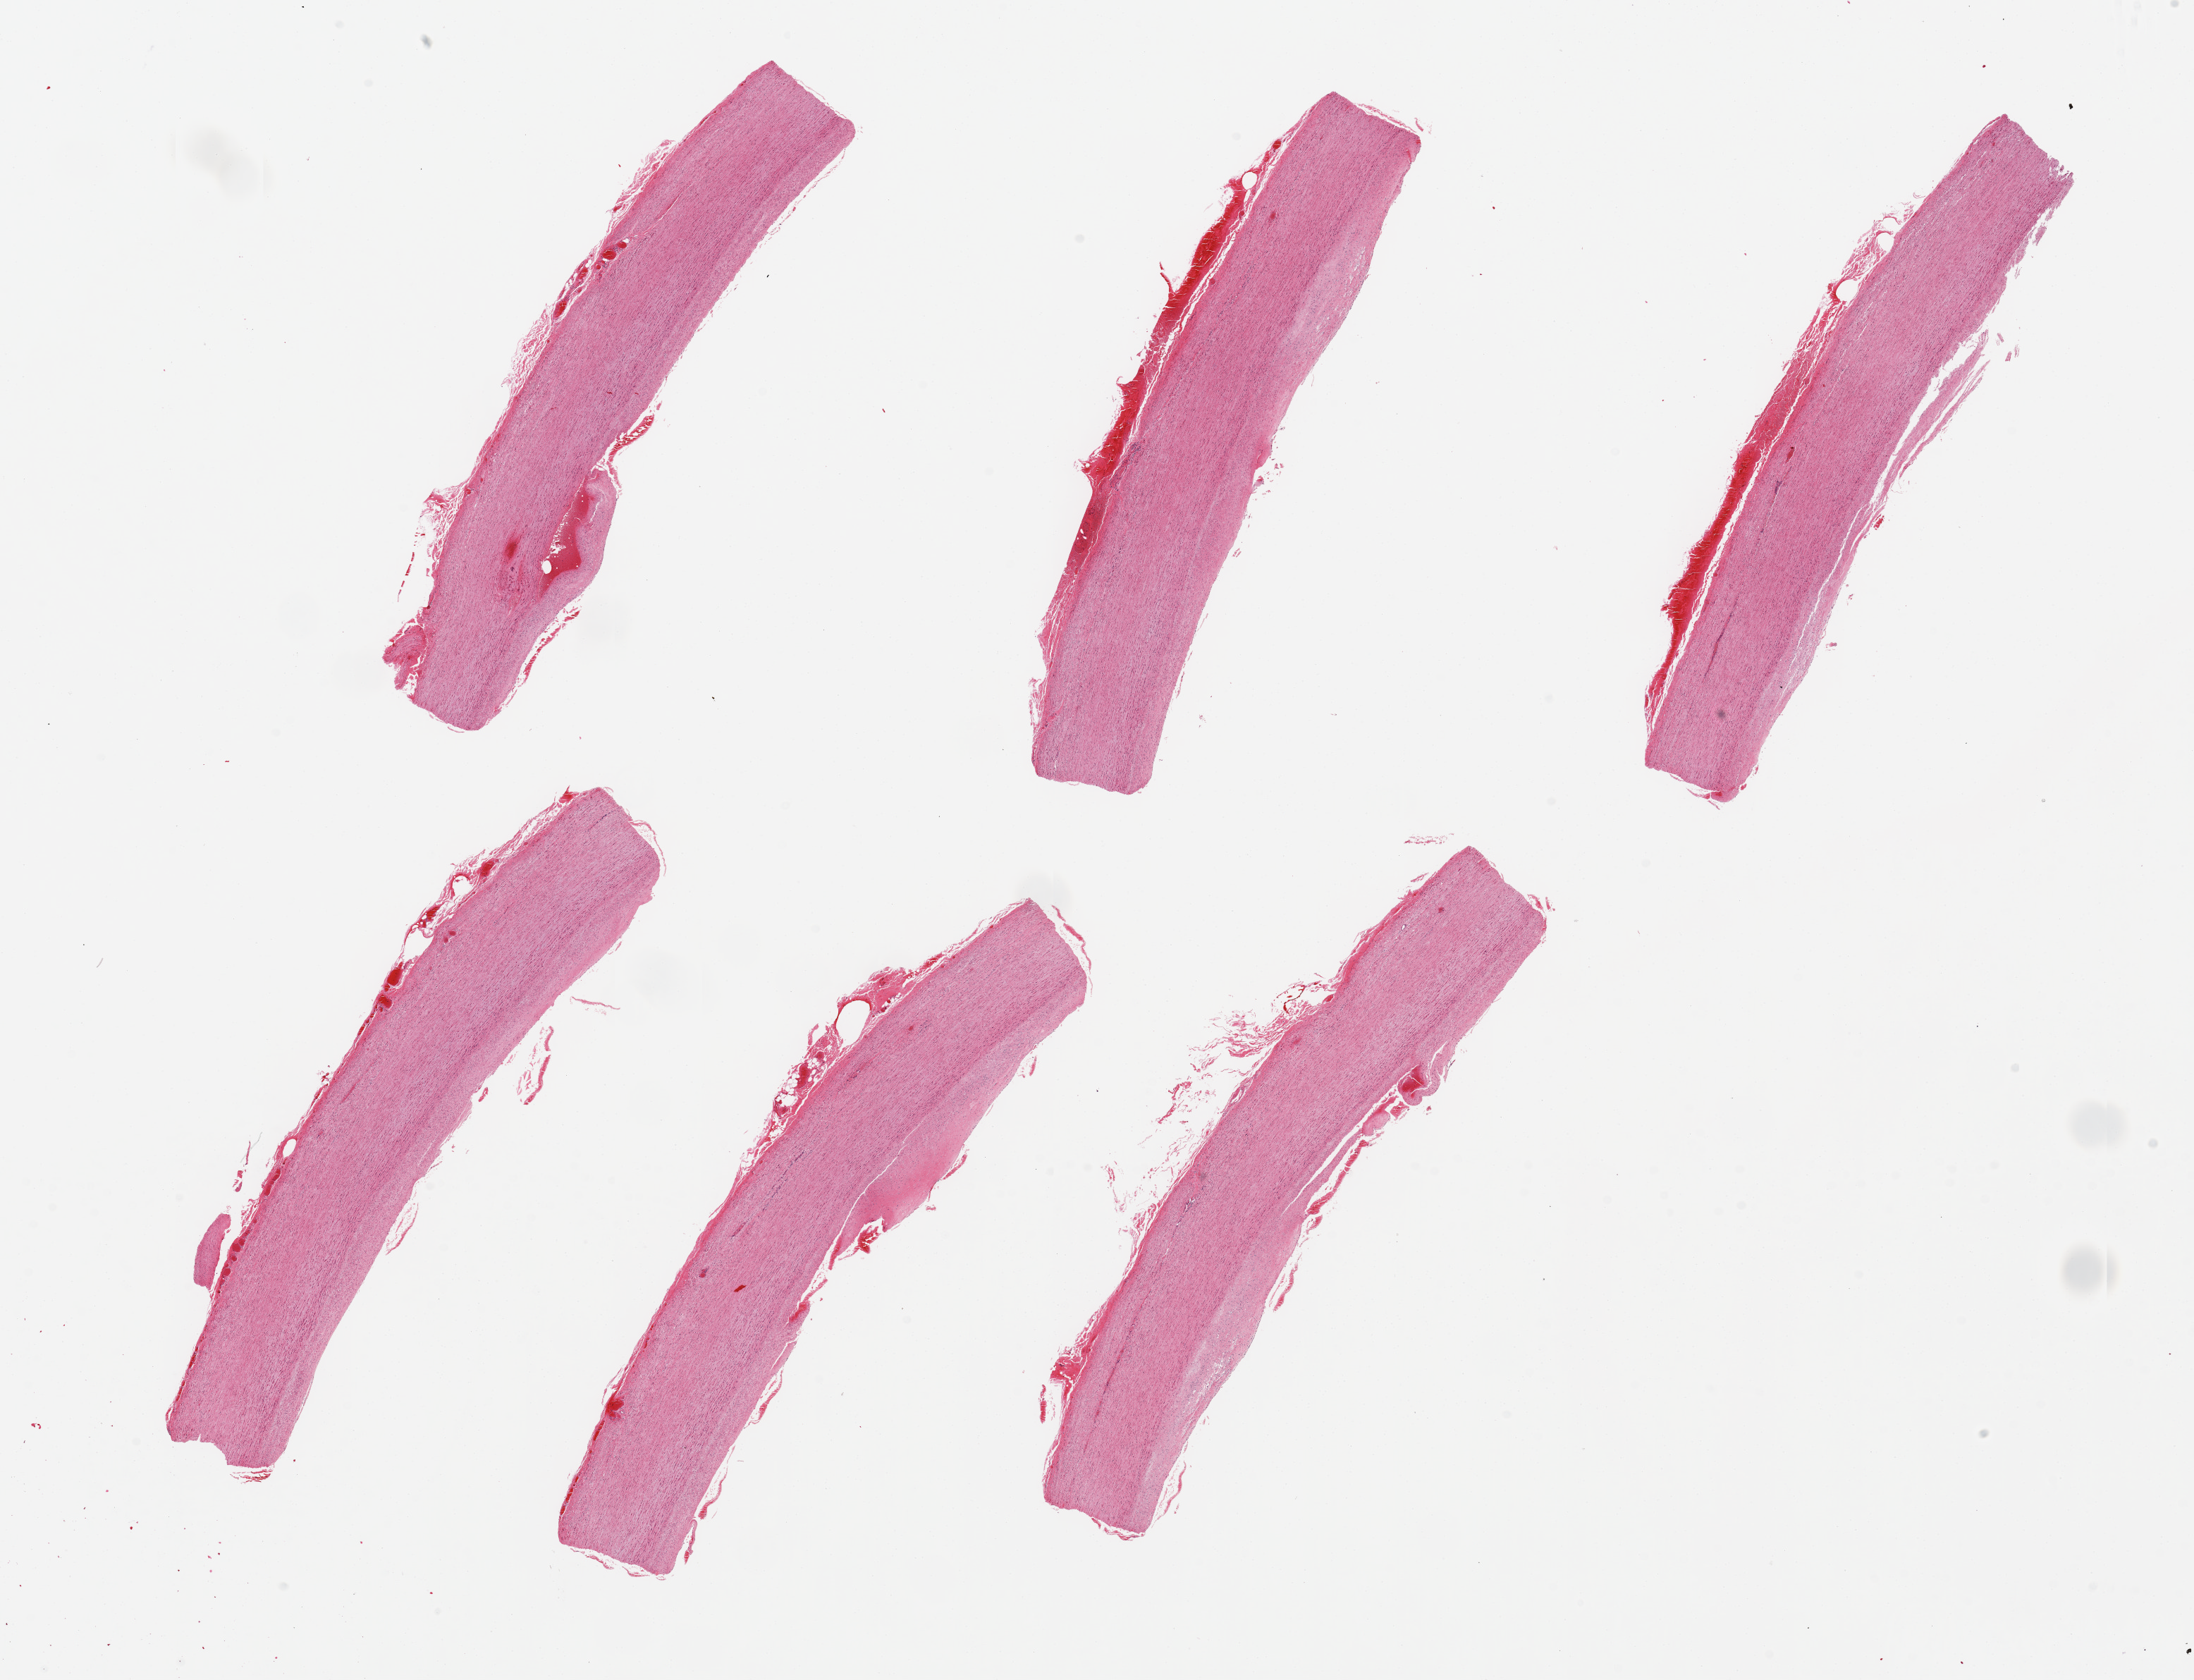
Digitized haematoxylin and eosin-stained section, low-resolution overview of the scanned area, about 24.6 x 18.8 mm (from a 20x scan); PAXgene-fixed, paraffin-embedded tissue; section of aorta (target tissue); donor tissue sample. Donor sex: male.
Pathologist's review note for this sample: 6 pieces, ~8x1.5mm.